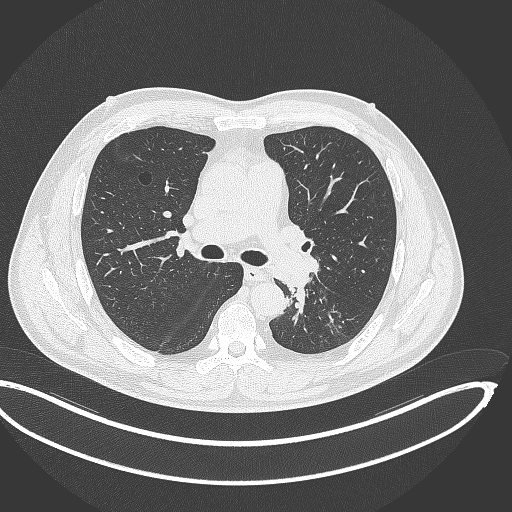
Chest CT, one axial slice; 120 kVp; lung window (W 1500 / L -600 HU); 1 mm slice thickness; 512 × 512 image matrix. Patient: male, 50 years. From the clinical record (not read from this slice): clinical TNM (as recorded): T2a N3 M0.
Outlined on this slice (rectangle marked by the reading radiologist):
- lung tumour (recorded histology: squamous cell carcinoma): bounding box (x1, y1, x2, y2) in pixels: (280, 271, 308, 325)